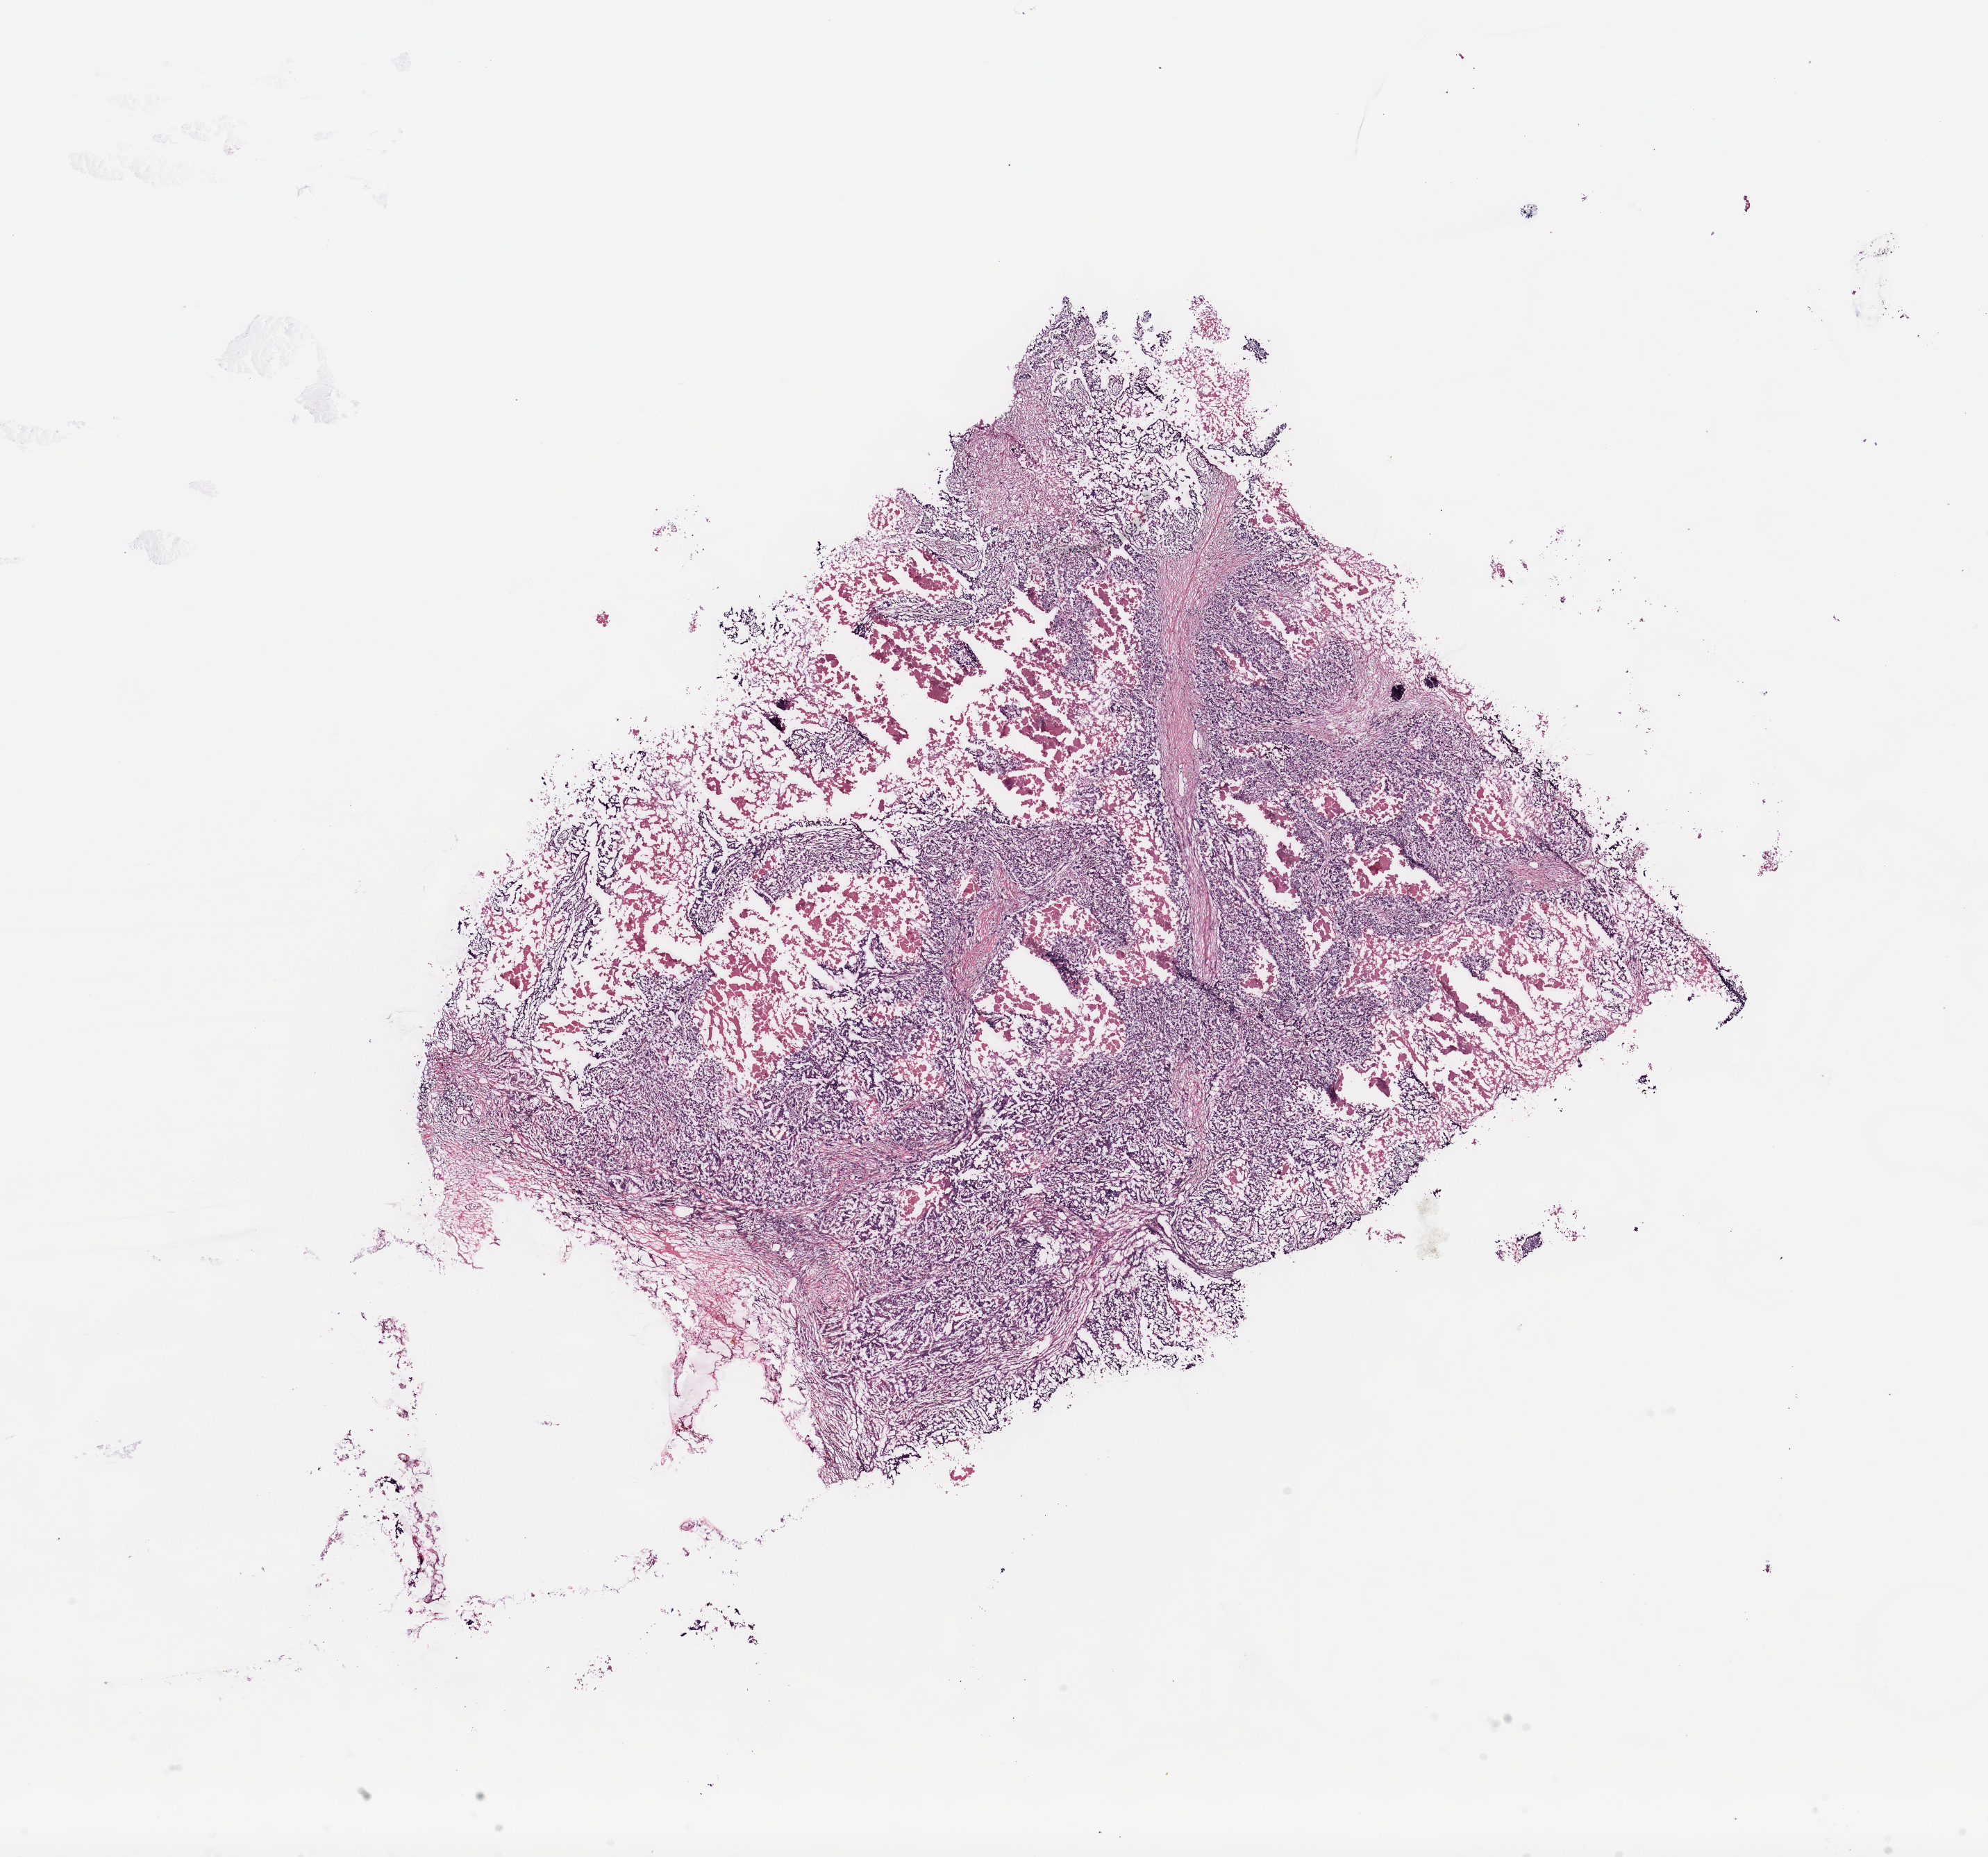
Hematoxylin and eosin (H&E) stained whole-slide image, low-resolution overview of the scanned area, about 22.6 x 21.2 mm, tumour tissue sample, breast. Patient: female, age 75 years.
Histologic diagnosis: Infiltrating duct carcinoma, NOS.